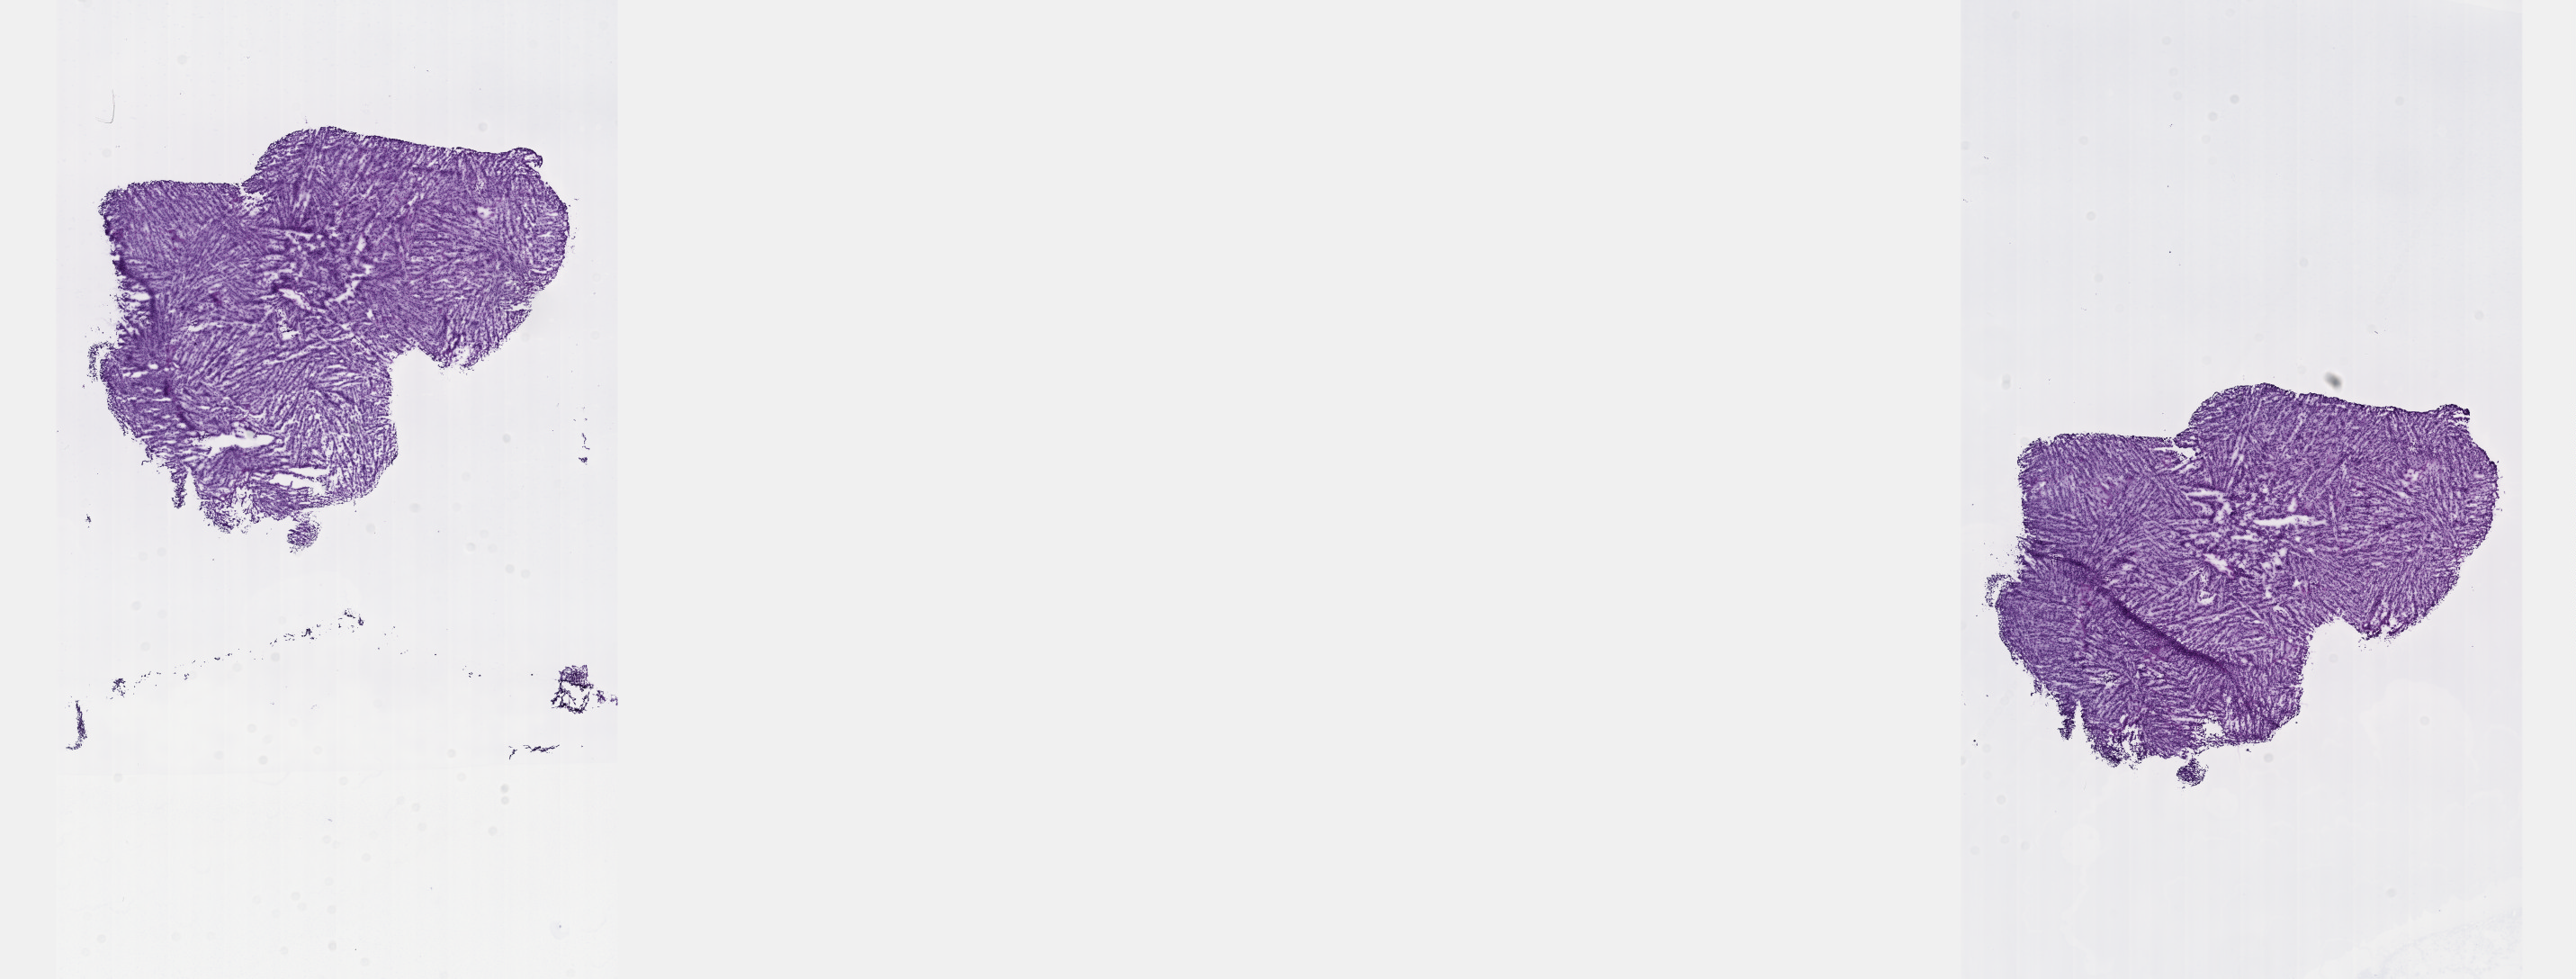
Hematoxylin and eosin (H&E) stained whole-slide image — a low-resolution overview of the entire scanned area, about 23.1 x 8.8 mm. Frozen section from the top of the tissue portion. Primary tumour sample from the uvea. Patient: male, age at initial diagnosis 73 years. Pathologist review of this section (percent, as recorded): tumour cells 100%, tumour nuclei 95%, normal cells 0%, stromal cells 0%, necrosis 0%. Infiltration values recorded for this section: lymphocyte infiltration 0%, monocyte infiltration 0%, neutrophil infiltration 0%.
AJCC pathologic stage: IIIA (7th edition). Pathologic diagnosis: Spindle cell melanoma, type B (overlapping lesion of eye and adnexa). TNM: T3b N0 M0.